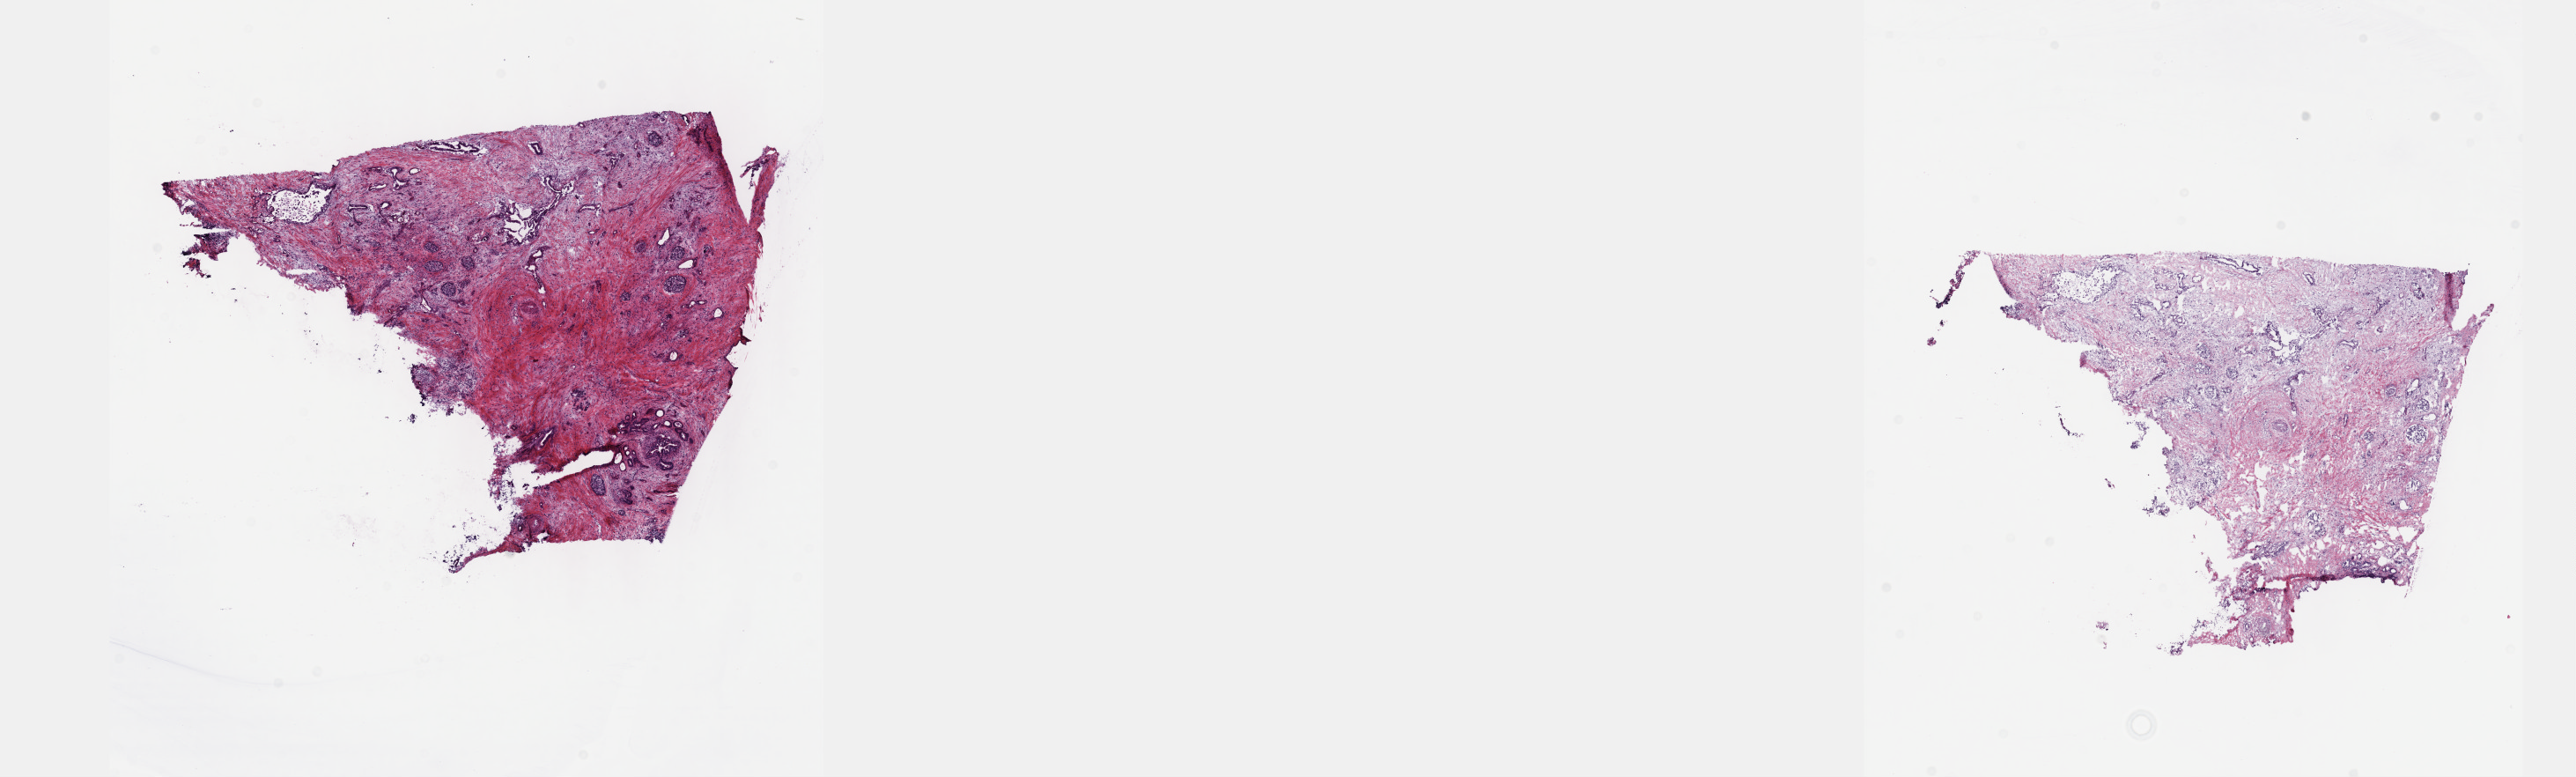
H&E whole-slide image, a low-resolution overview of the entire scanned area, about 23.6 x 7.1 mm; frozen section from the top of the tissue portion; pancreas, primary tumour sample. Female patient; age at initial diagnosis 57 years. Histologic grade: G2 (moderately differentiated). Composition of this section per pathologist review: tumour cells 60%, tumour nuclei 60%, normal cells 10%, stromal cells 30%, necrosis 0%. Inflammatory infiltration, as recorded: lymphocyte infiltration 70%, monocyte infiltration 10%, neutrophil infiltration 10%.
Diagnosis: Infiltrating duct carcinoma, NOS (head of pancreas). AJCC pathologic stage: IIB (7th edition). Lymph nodes positive (case pathology): 7 of 30 examined.